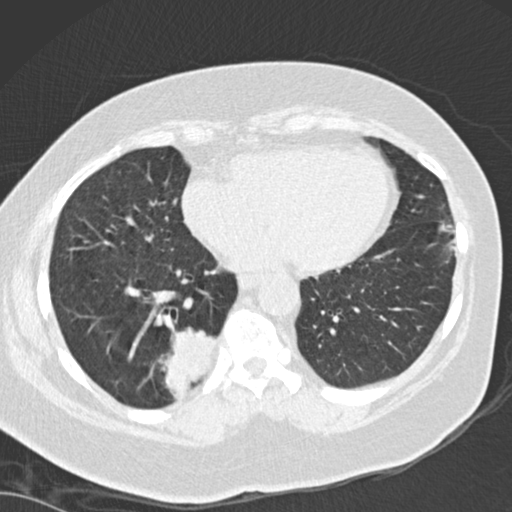
Low-dose screening chest CT, one axial slice. Position 59 of 162 along the scan axis. 120 kVp. Lung window (W 1500 / L -600 HU). 512 × 512 image matrix, field of view 328 × 328 mm.
Annotated regions visible in this slice (expert manual segmentation):
- lesion 1 (tumor, lower lobe of right lung): box from (x=164, y=327) to (x=218, y=401) px